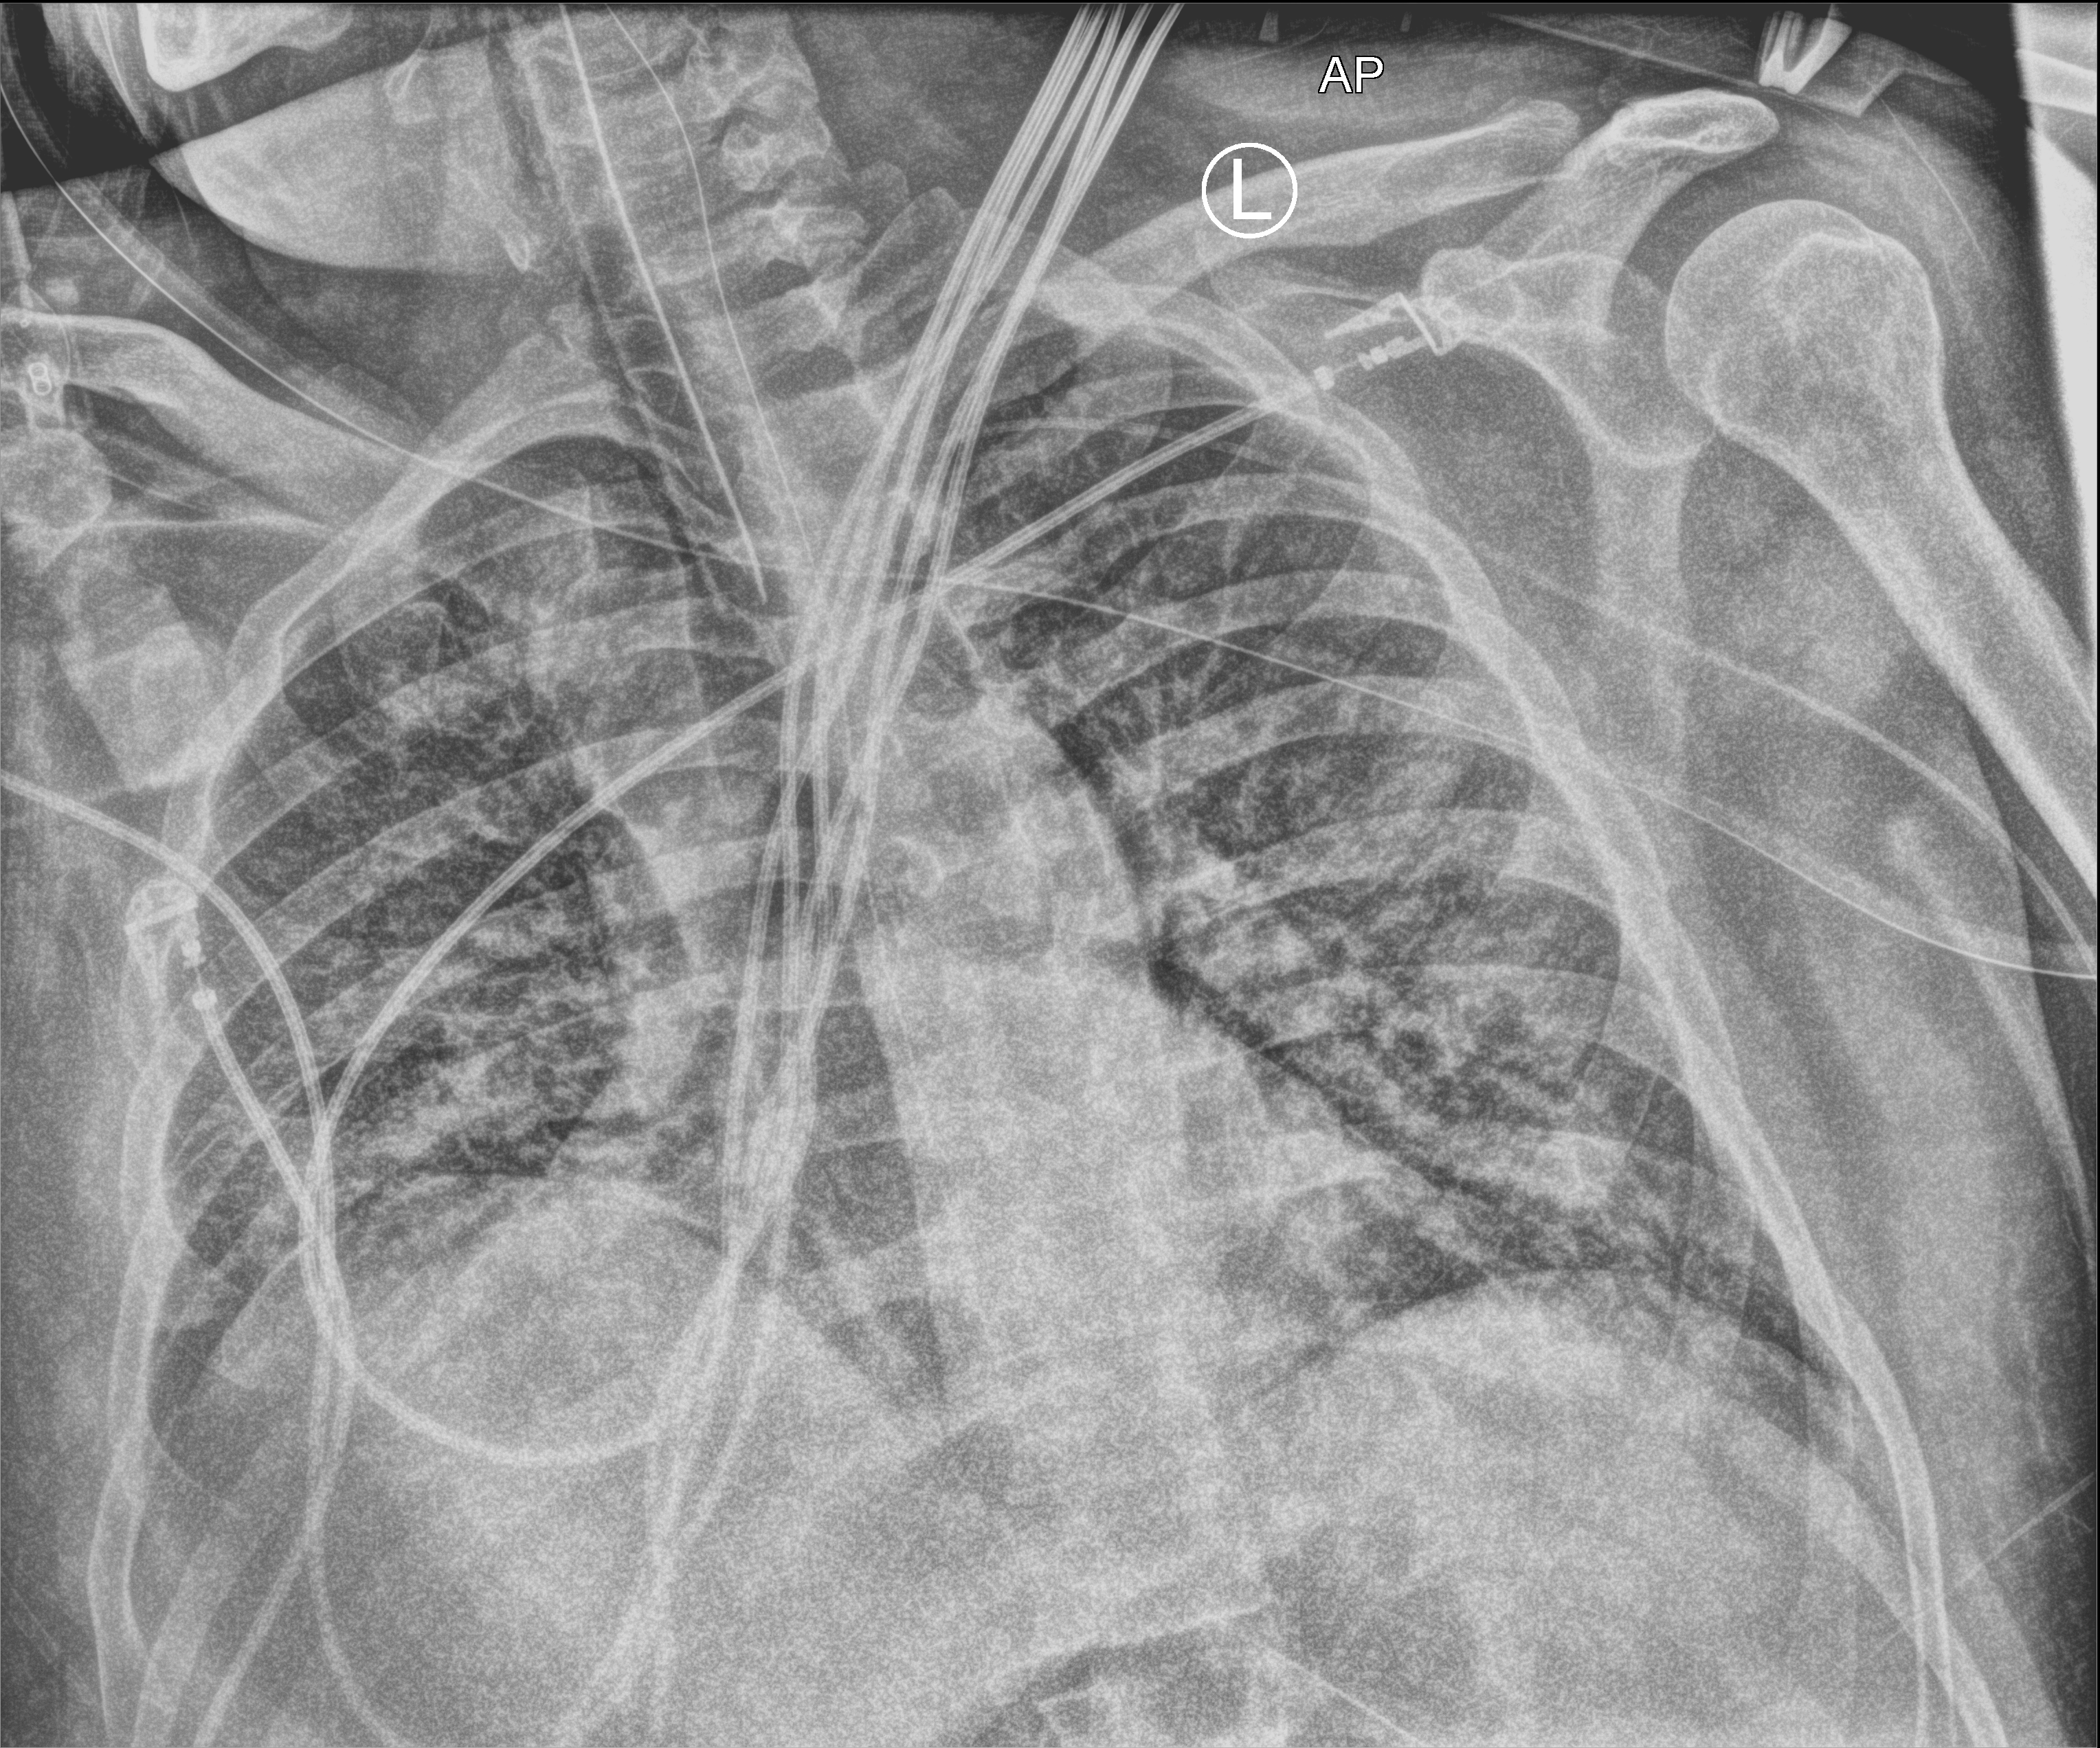
Chest X-ray (portable). Male patient hospitalised with COVID-19, age 18–59 years.
Hospital-stay facts (about this admission, not read from this image; timing relative to this image not recorded): mechanically ventilated during this hospital stay: yes; admitted to intensive care during this hospital stay: yes.